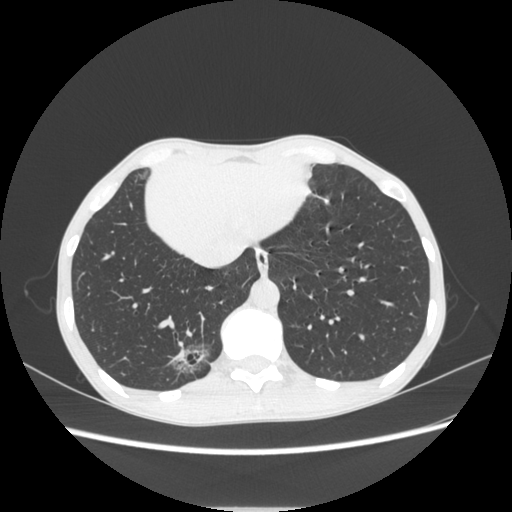
Chest CT, one axial slice; position 71 of 272 along the scan axis; reconstruction kernel STANDARD; lung window (W 1500 / L -600 HU); 512 × 512 image matrix, field of view 350 × 350 mm. Patient: female, 51 years. From the clinical record (not read from this slice): clinical TNM (as recorded): T1c N0 M0; histopathological grade: G2-3.
Annotated regions visible in this slice (rectangle marked by the reading radiologist):
- lung tumour (recorded histology: adenocarcinoma): bounding box <160,335,215,386> (left, top, right, bottom; pixels)